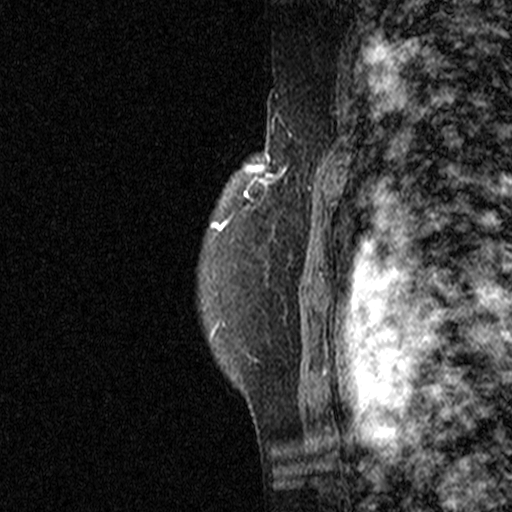
Breast MRI (dynamic contrast-enhanced), one sagittal slice; slice 35 of 44 in the series (ordered by position); dynamic contrast-enhanced study with each time point stored as its own series, time point 2 of 3 at this slice position (early post-contrast, ordered by acquisition time); 1.5 T; TE 4.5 ms, TR 11 ms; 512 × 512 image matrix, field of view 200 × 200 mm. Female patient, age 49 years. From the clinical record (not read from this slice): setting: breast cancer imaged before/during neoadjuvant chemotherapy; receptor status: triple-negative.
Outlined on this slice (semi-automatic segmentation, software-assisted and operator-edited):
- analysis volume of interest (the breast-tissue region the enhancement analysis was run in; not a lesion): bounding box [x1, y1, x2, y2] px = [268, 122, 331, 227]
- tumour enhancement mask (voxels above the 90 % enhancement threshold inside the analysis volume of interest): [269, 168, 322, 214]